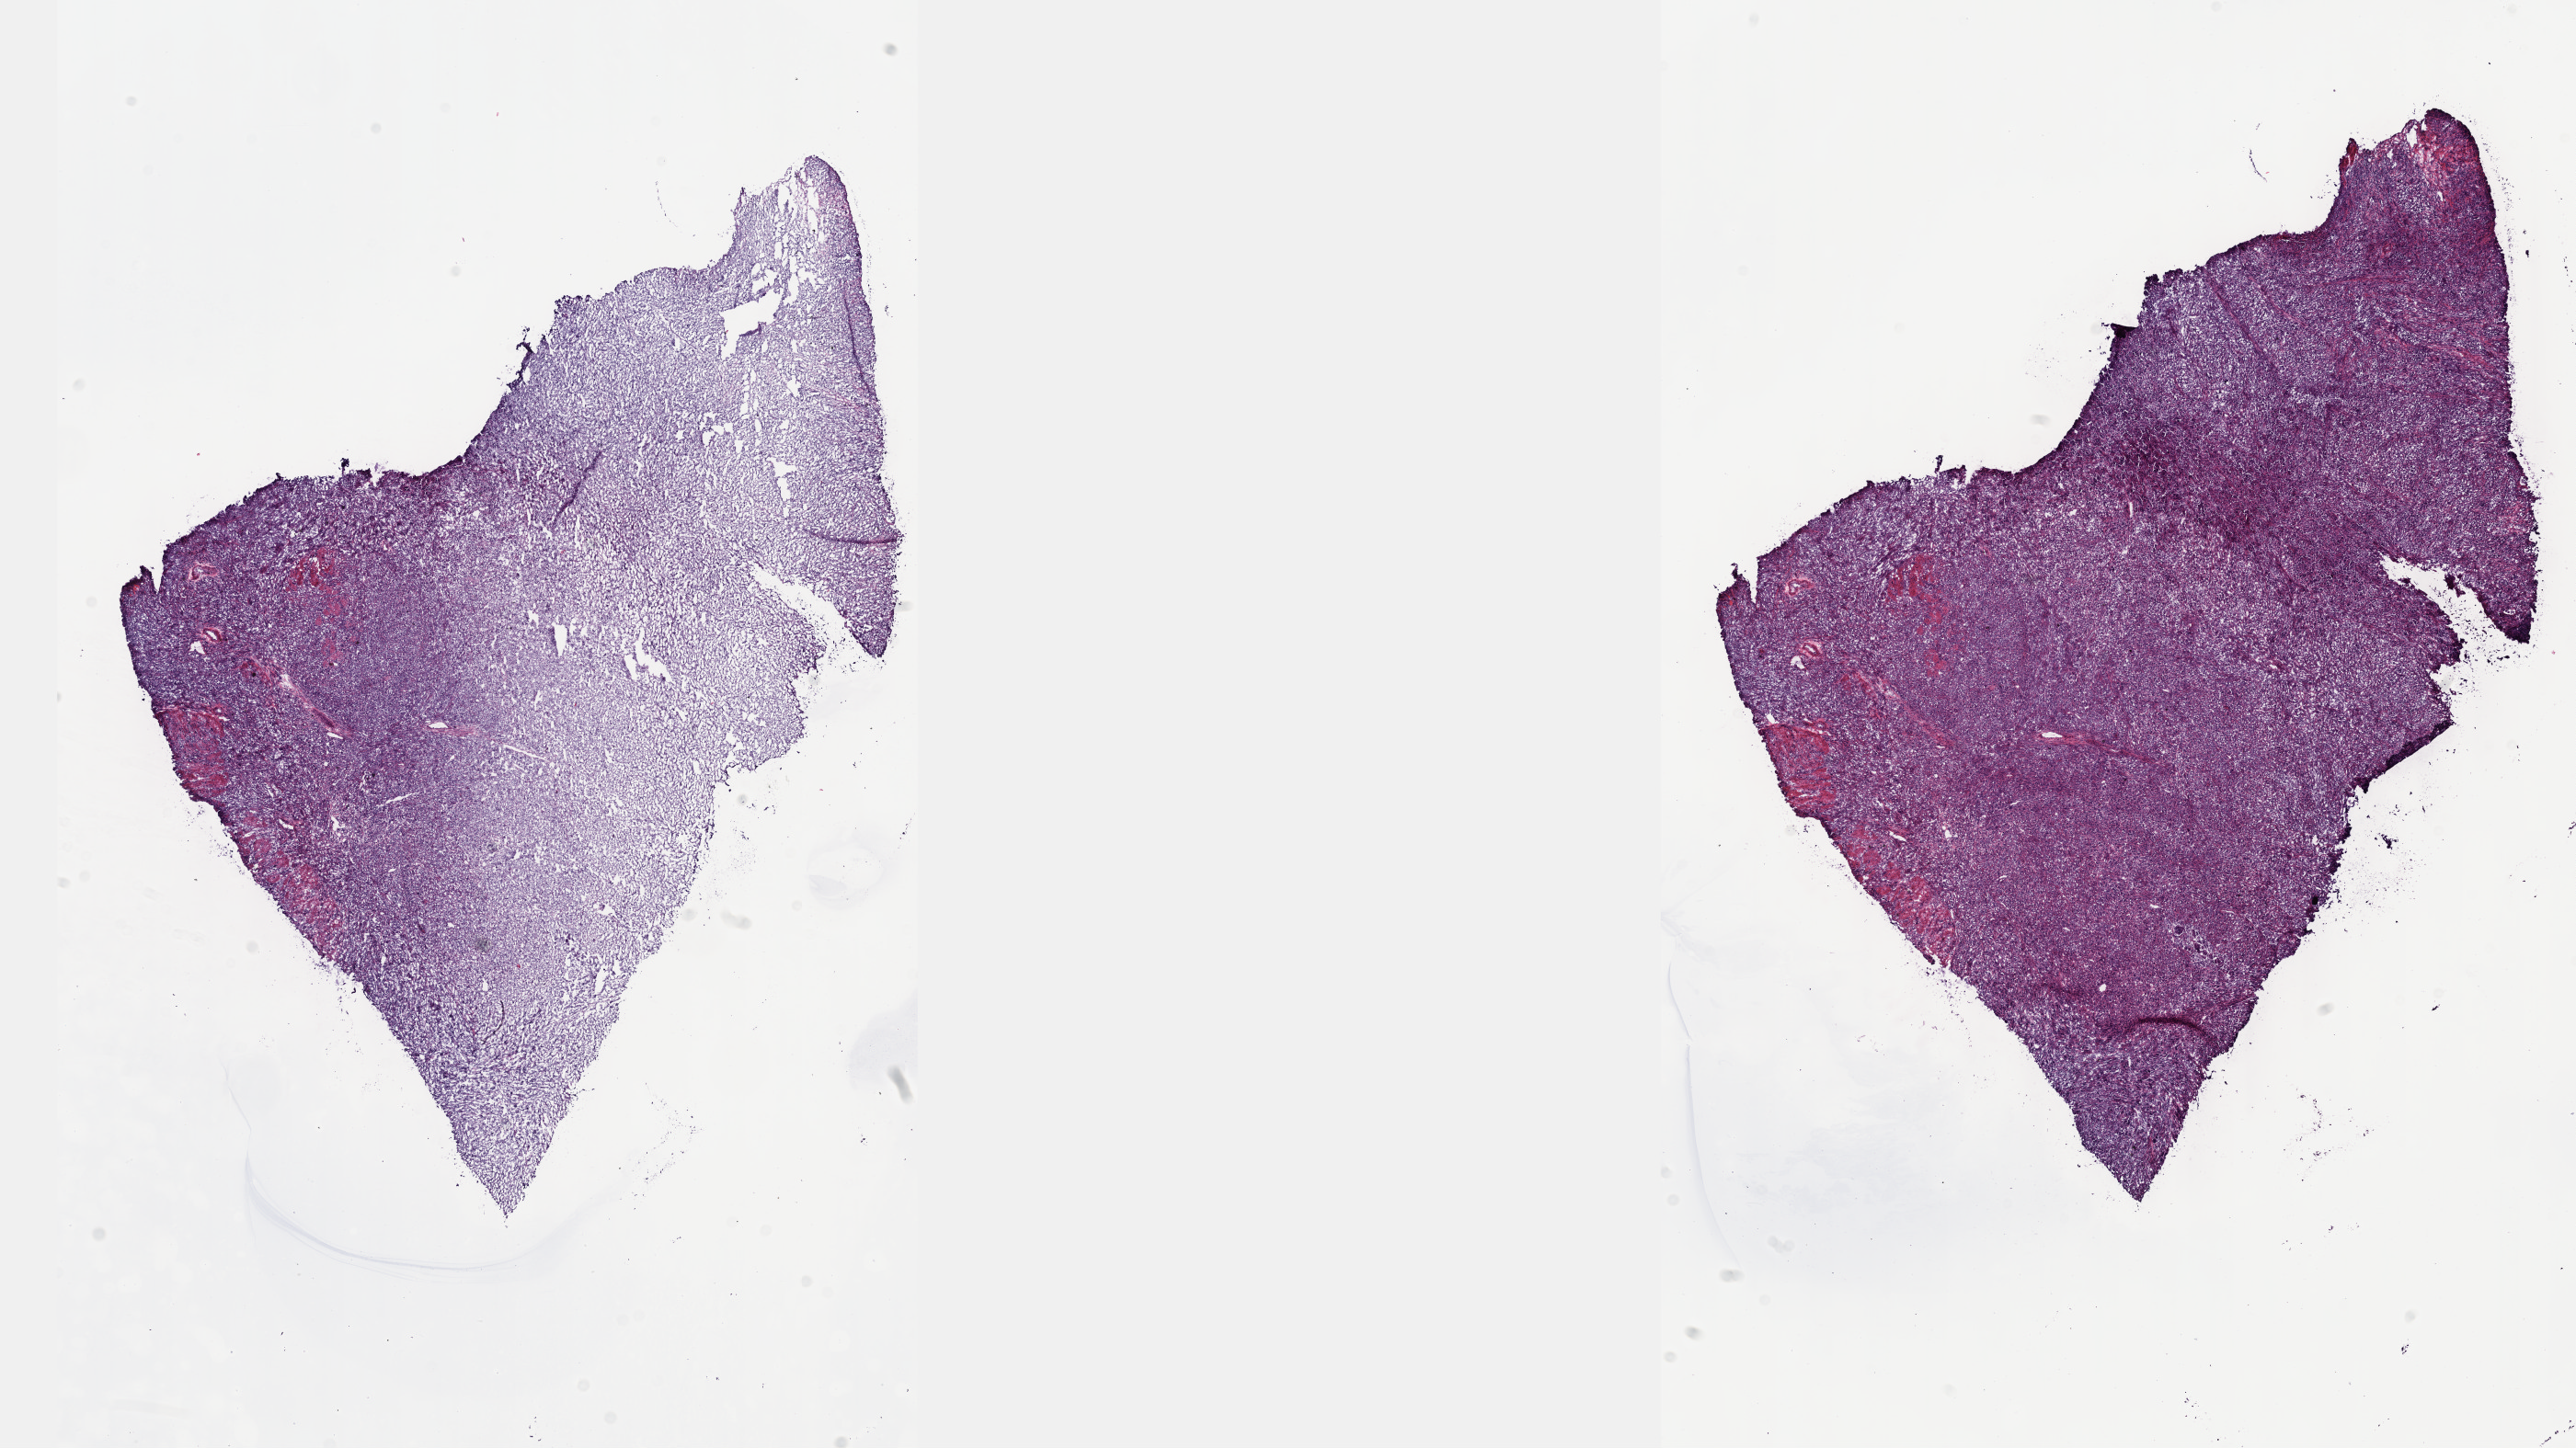
Digitized Hematoxylin and eosin (H&E) stained tissue section (whole slide), whole scanned area (about 22.6 x 12.7 mm) shown as a low-resolution overview, frozen section, bladder, primary tumour sample. Patient: male, age at initial diagnosis 71 years. Histologic grade: high grade. Slide review estimates, as recorded: tumour cells 90%, tumour nuclei 95%, normal cells 0%, stromal cells 10%, necrosis 0%. Inflammatory infiltration, as recorded: lymphocyte infiltration 0%, monocyte infiltration 0%, neutrophil infiltration 0%.
- histologic diagnosis: Transitional cell carcinoma
- AJCC pathologic stage: III